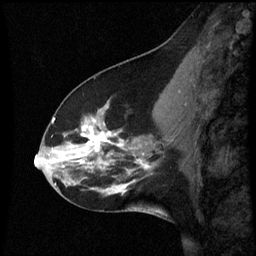
Breast MRI (dynamic contrast-enhanced), one sagittal slice. Slice 25 of 60 in the series (ordered by position). Dynamic contrast-enhanced series, image 2 of 3 at this slice position (ordered by acquisition). 1.5 T. TE 4.2 ms, TR 8.9 ms. 2 mm slice thickness. 256 × 256 image matrix, field of view 200 × 200 mm. Patient: female, 45 years. Case-level facts recorded for this patient, not image findings: setting: breast cancer imaged before/during neoadjuvant chemotherapy; receptor status: HR-positive, HER2-negative.
Outlined on this slice (semi-automatically segmented with operator editing):
- analysis volume of interest (the breast-tissue region the enhancement analysis was run in; not a lesion): box from (x=46, y=94) to (x=171, y=205) px
- tumour enhancement mask (voxels above the 70 % enhancement threshold inside the analysis volume of interest): (x=52, y=118)–(x=149, y=183)